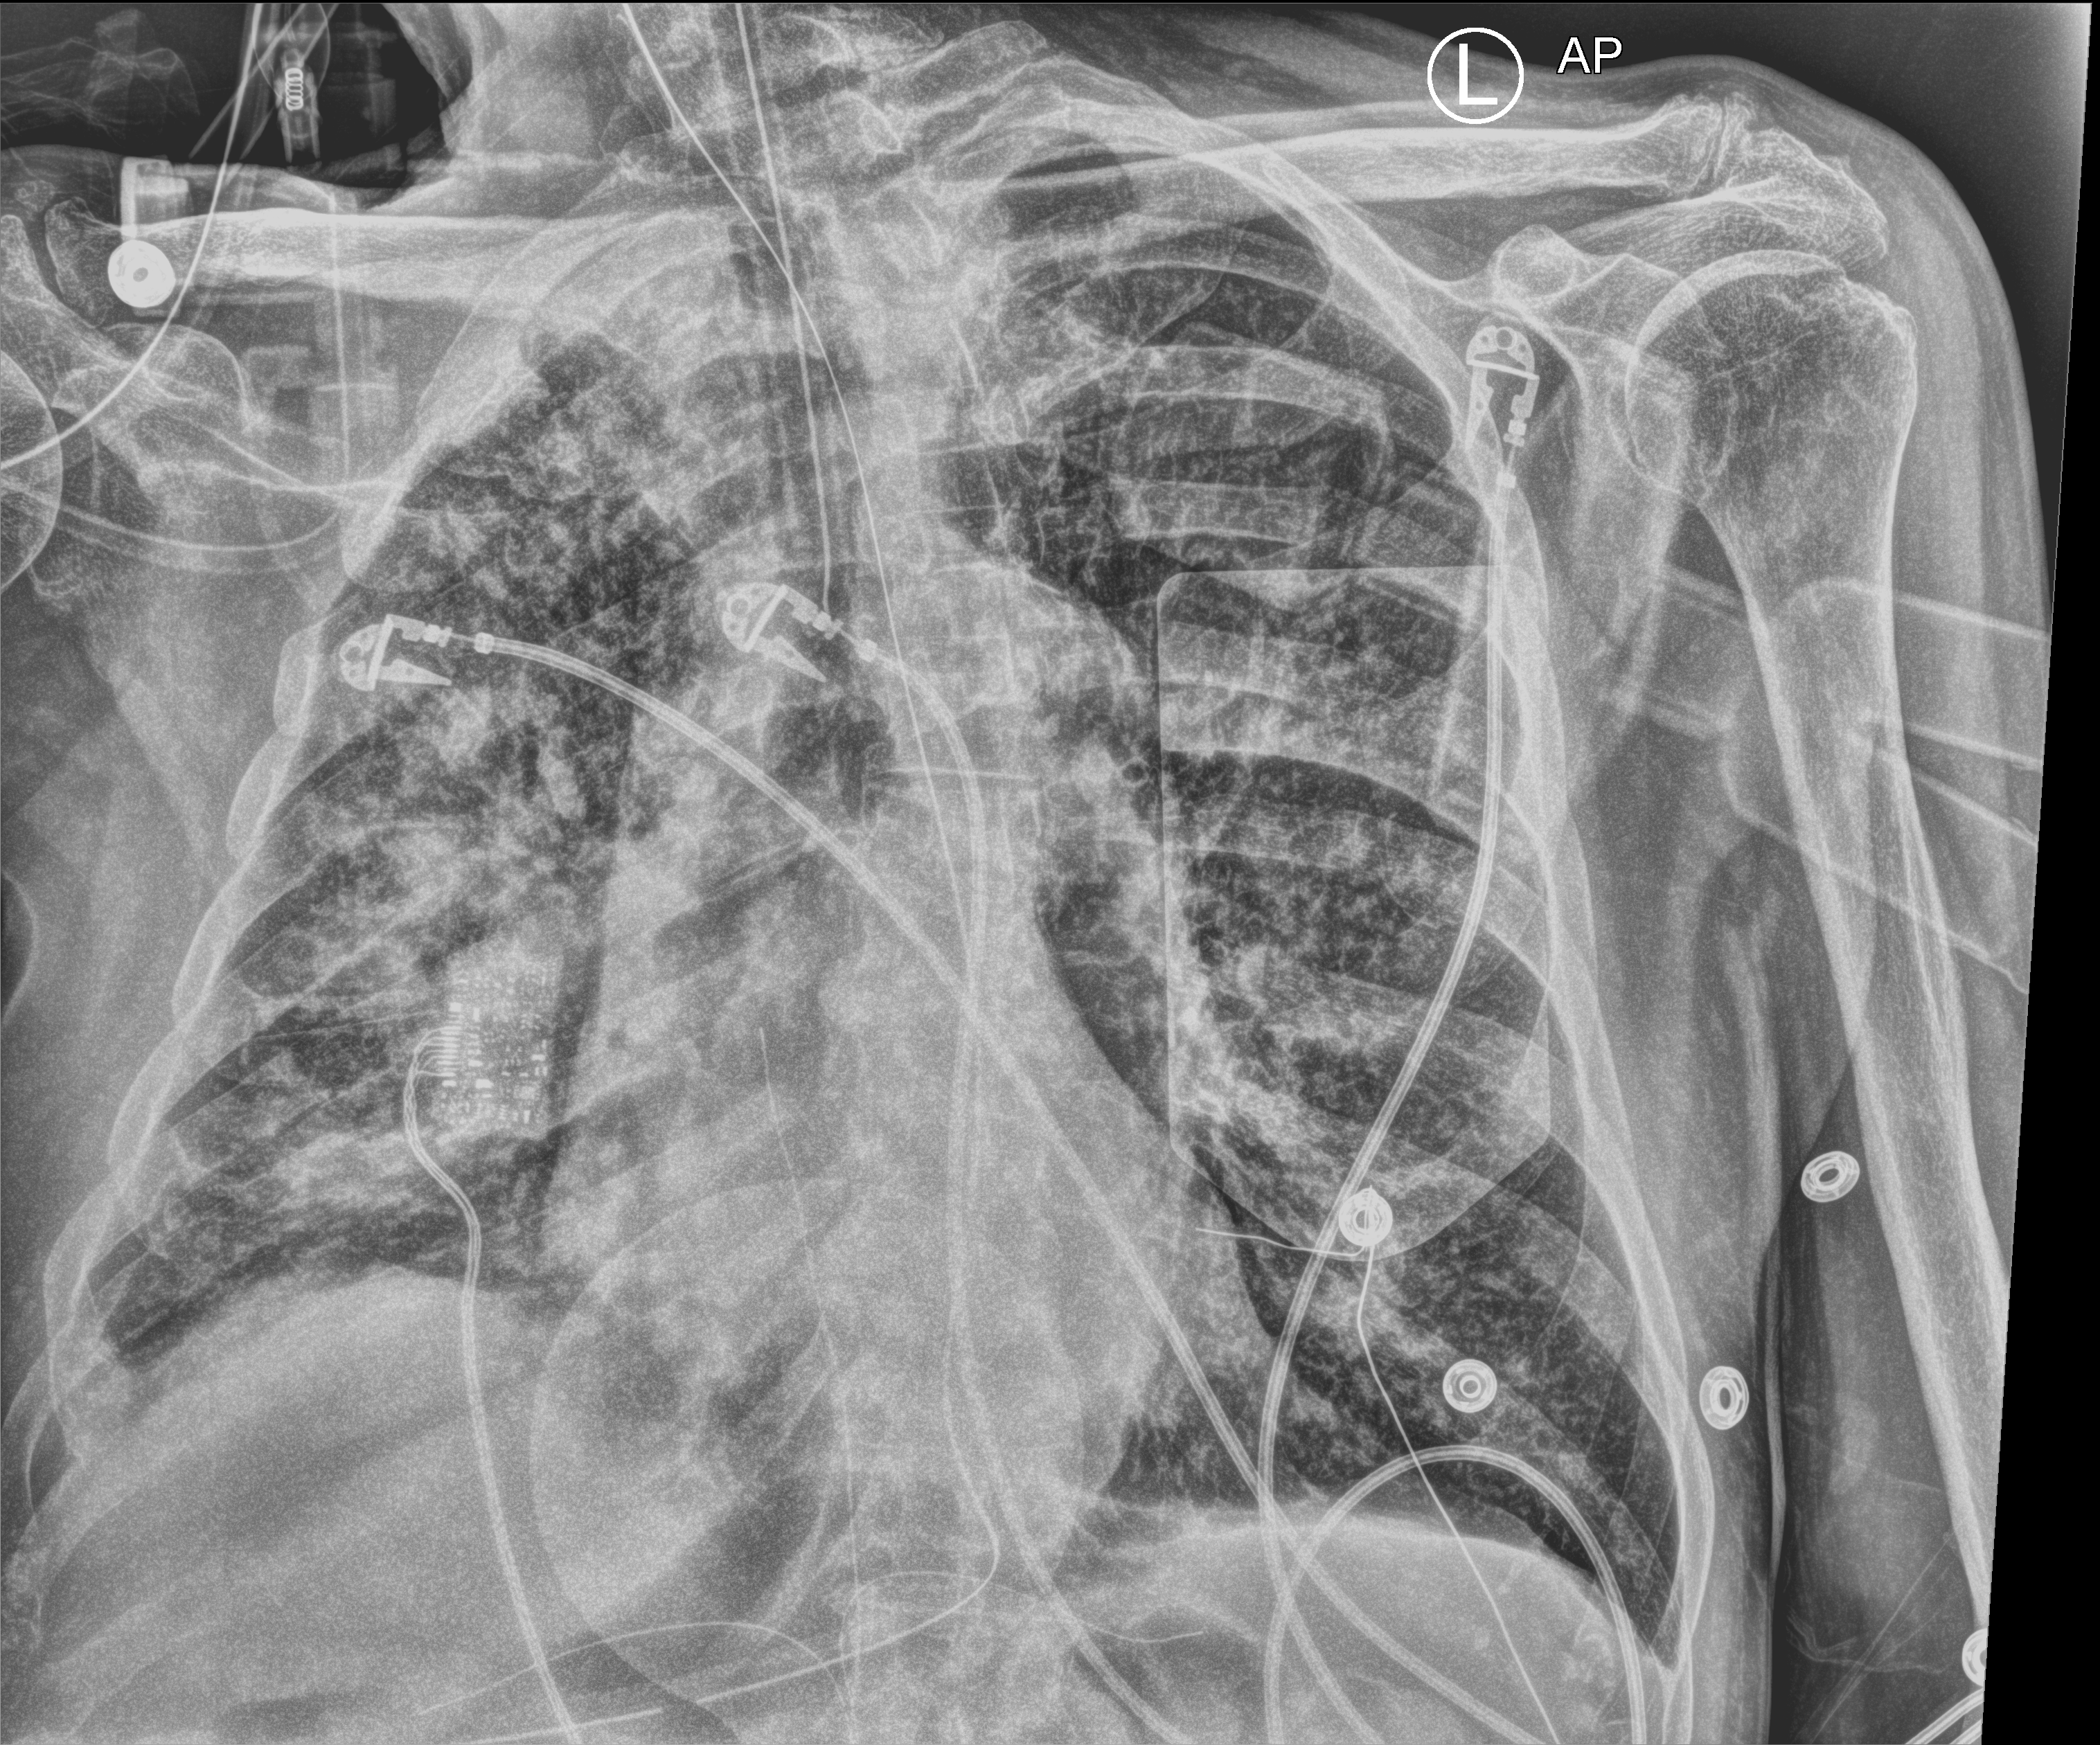
Bedside chest radiograph (computed radiography); anteroposterior (AP) projection. Male patient hospitalised with COVID-19, age 75–90 years.
From the hospital-stay record, not from the radiograph (when in the stay this image was taken is not recorded):
- admitted to intensive care during this hospital stay: yes
- mechanically ventilated during this hospital stay: yes